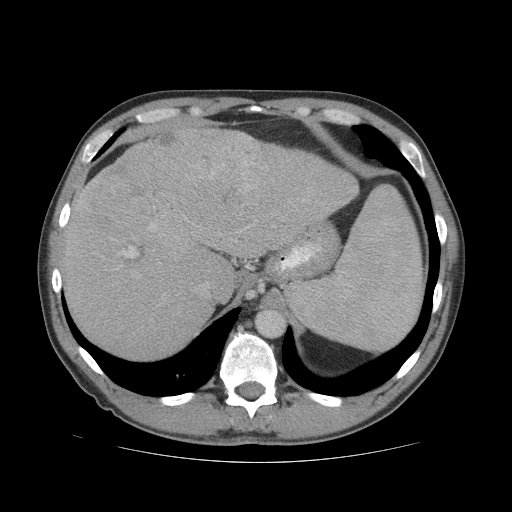
Contrast-enhanced abdominal CT (liver protocol), one axial slice. Position 54 of 81 along the scan axis. 140 kVp. Soft-tissue window (W 400 / L 40 HU). 2.5 mm slice thickness. 512 × 512 image matrix, field of view 400 × 400 mm. From the clinical record (not read from this slice): diagnosis: hepatocellular carcinoma (patient treated with transarterial chemoembolisation; whether this scan precedes or follows treatment is not stated here); TNM stage (as recorded): Stage-IVB.
Outlined on this slice (semi-automatically segmented with operator editing):
- liver parenchyma outside the tumour (the mass and vessels are separate outlines, so this box may not span the whole liver): bounding box <62,128,358,360> (left, top, right, bottom; pixels)
- mass: <79,126,264,218>
- liver vessels: <111,185,304,258>